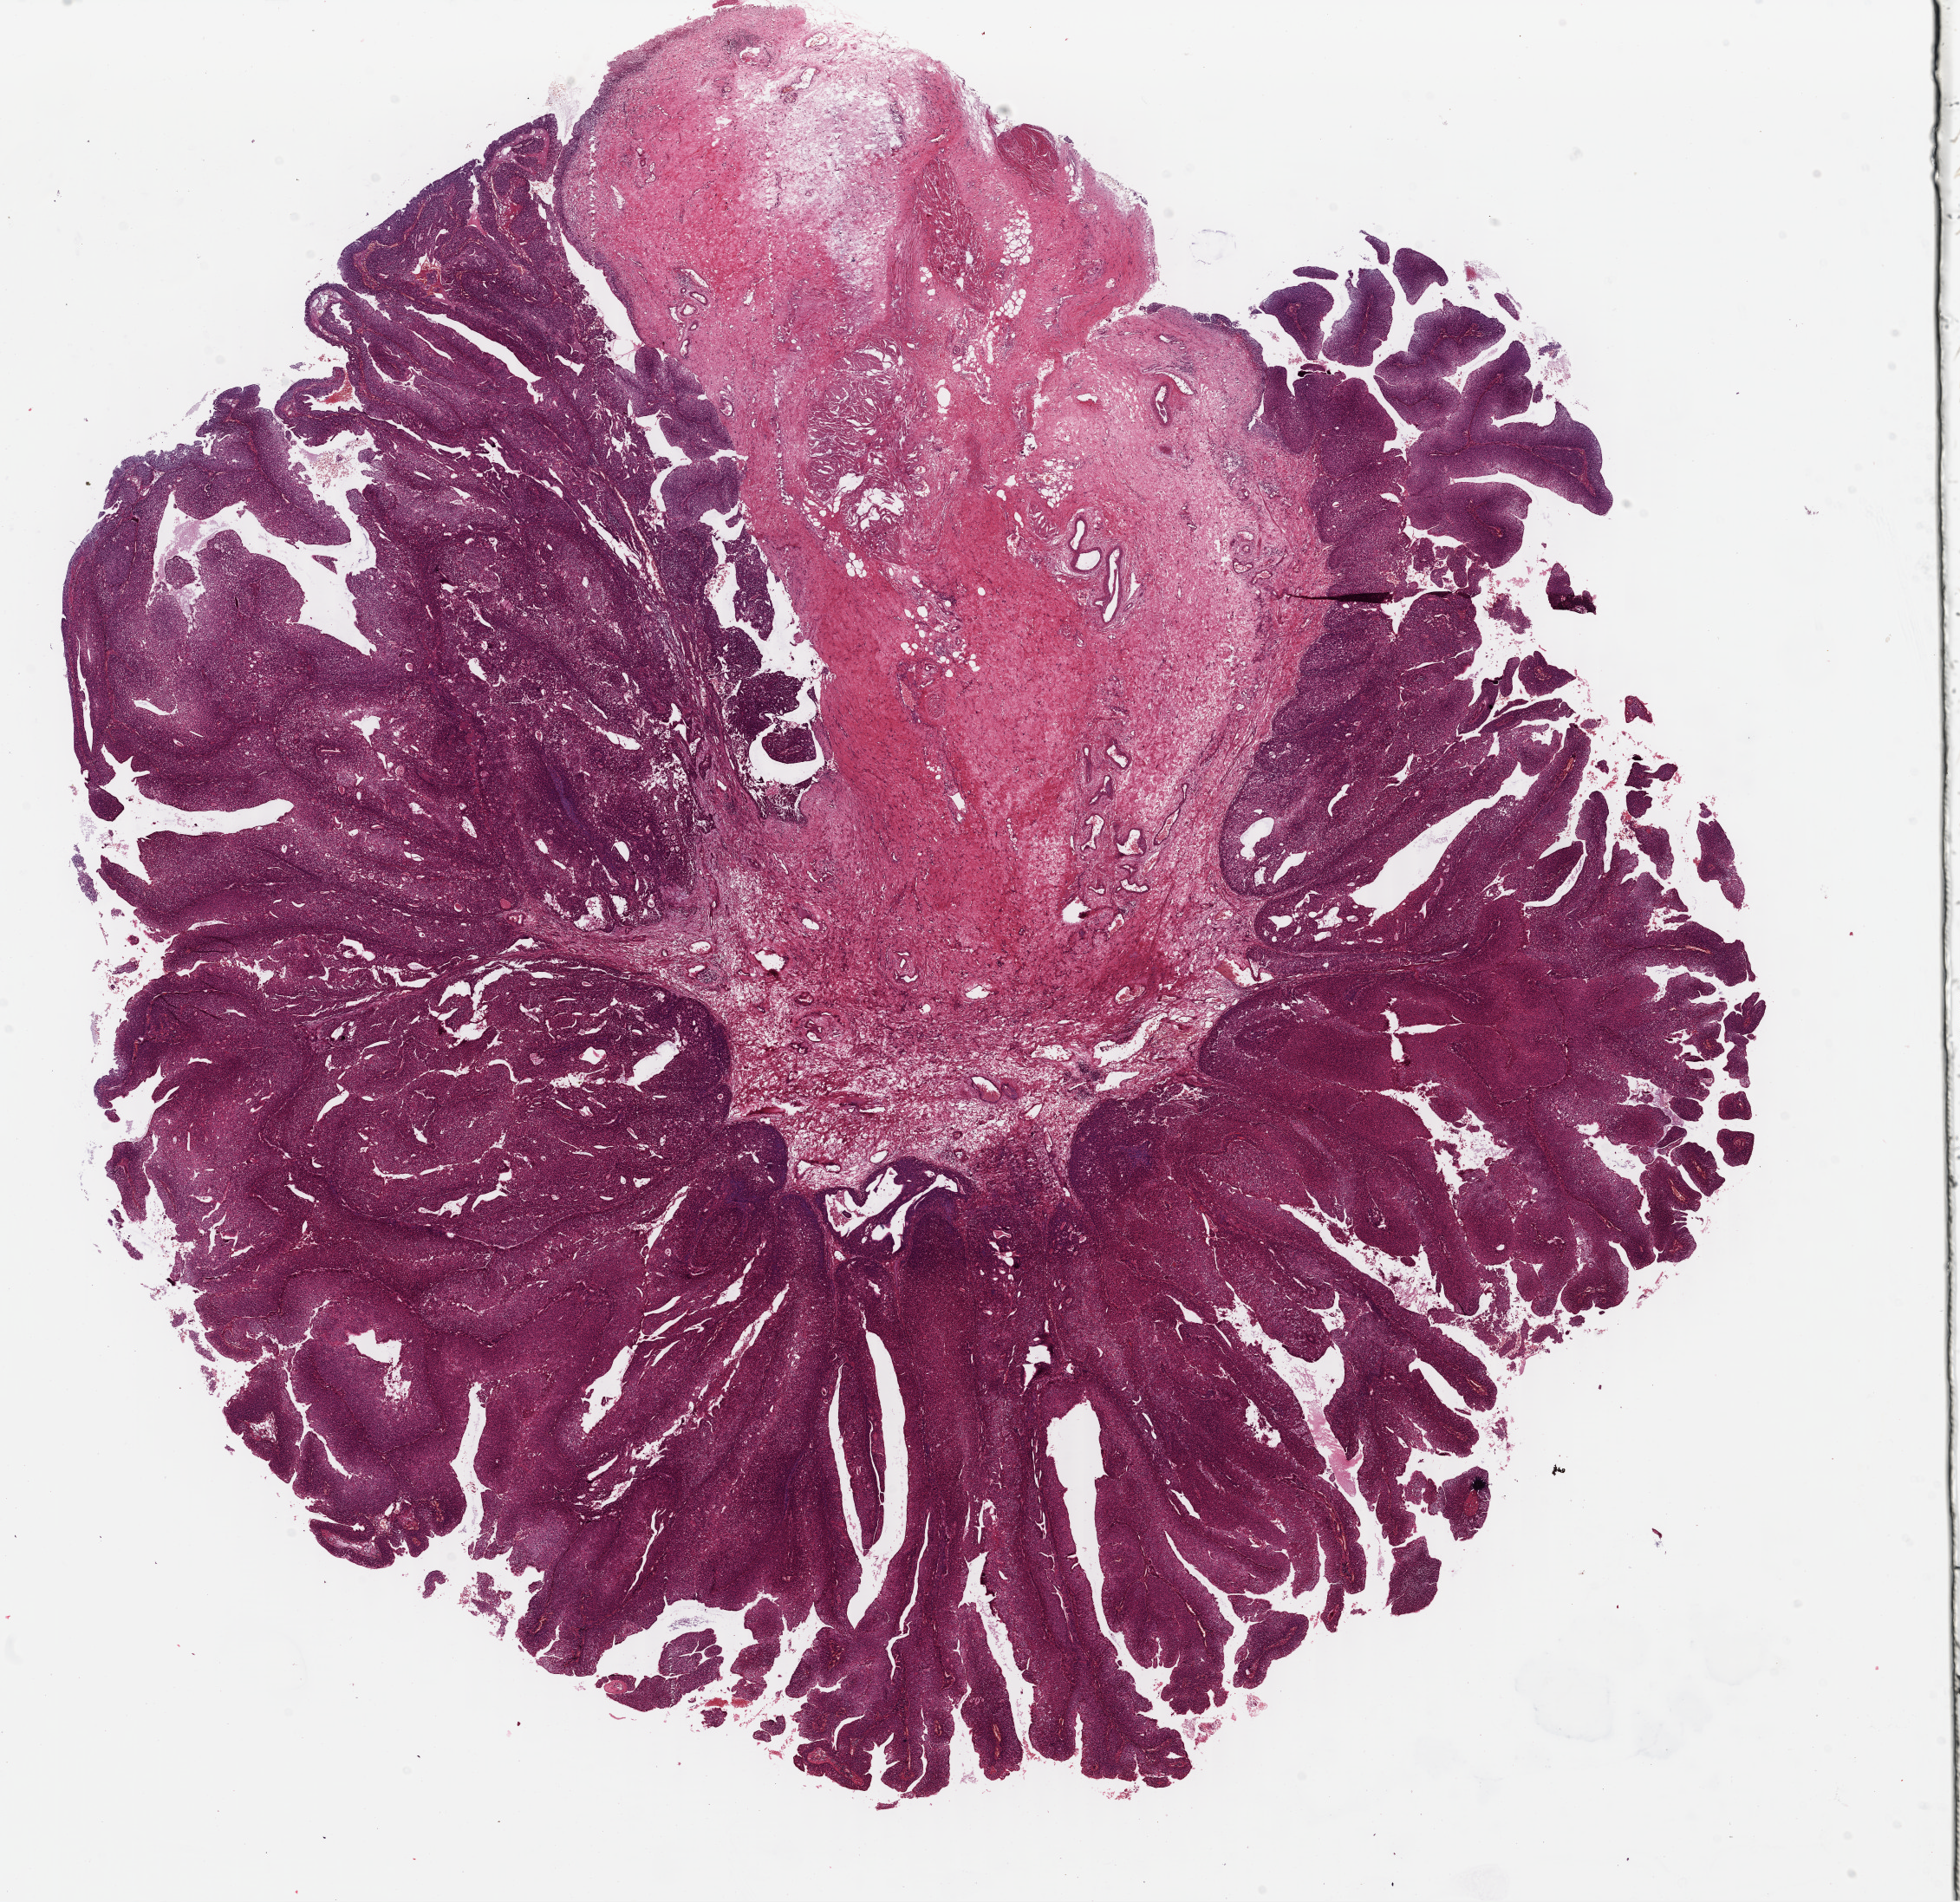
Digitized Hematoxylin and eosin (H&E) stained tissue section (whole slide) — whole scanned area (about 17.8 x 17.2 mm, slide scanned at 40x) shown as a low-resolution overview; formalin-fixed paraffin-embedded (FFPE) diagnostic section; bladder, primary tumour sample. Male patient; age at initial diagnosis 75 years. Histologic grade: low grade.
* diagnosis: Papillary transitional cell carcinoma
* AJCC pathologic stage: II